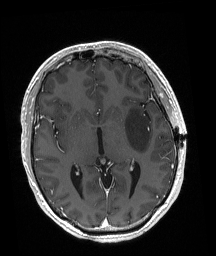
Brain MRI from a brain-tumour surgery series, one axial slice; position 103 of 192 along the scan axis; T1-weighted post-contrast; 1 mm slice thickness; 216 × 256 image matrix, field of view 211 × 250 mm. Case-level facts recorded for this patient, not image findings: histopathology: Astrocytoma; WHO grade: 3; IDH mutation: yes.
Annotated regions visible in this slice (outlined manually by an expert reader):
- tumour: bounding box <125,109,152,152> (left, top, right, bottom; pixels)